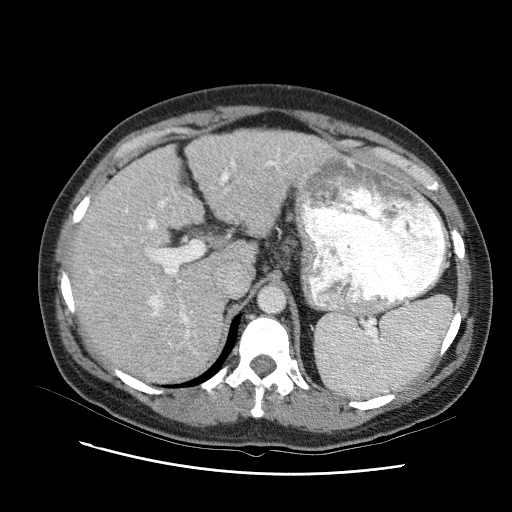
Contrast-enhanced abdominal CT (liver protocol), one axial slice; reconstruction kernel STANDARD; 120 kVp; one of 2 acquisitions stored at this slice position; soft-tissue window (W 400 / L 40 HU); 2.5 mm slice thickness; 512 × 512 image matrix, field of view 360 × 360 mm. Case-level facts recorded for this patient, not image findings: diagnosis: hepatocellular carcinoma (patient treated with transarterial chemoembolisation; whether this scan precedes or follows treatment is not stated here); TNM stage (as recorded): Stage-I; Child-Pugh class: B; tumour differentiation: moderately differentiated.
Structures marked on this image (semi-automatic segmentation, software-assisted and operator-edited):
- abdominal aorta: box from (x=258, y=285) to (x=284, y=312) px
- liver parenchyma outside the tumour (the mass and vessels are separate outlines, so this box may not span the whole liver): (x=70, y=126)–(x=337, y=372)
- liver vessels: (x=128, y=155)–(x=294, y=353)